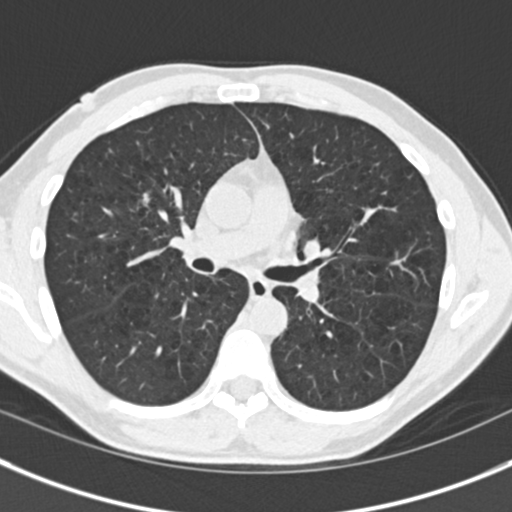
Low-dose screening chest CT, one axial slice; position 98 of 175 along the scan axis; reconstruction kernel B30f; lung window (W 1500 / L -600 HU); 512 × 512 image matrix, field of view 306 × 306 mm.
Structures marked on this image (expert manual segmentation):
- lesion 1 (tumor, upper lobe of right lung): box from (x=143, y=193) to (x=150, y=206) px